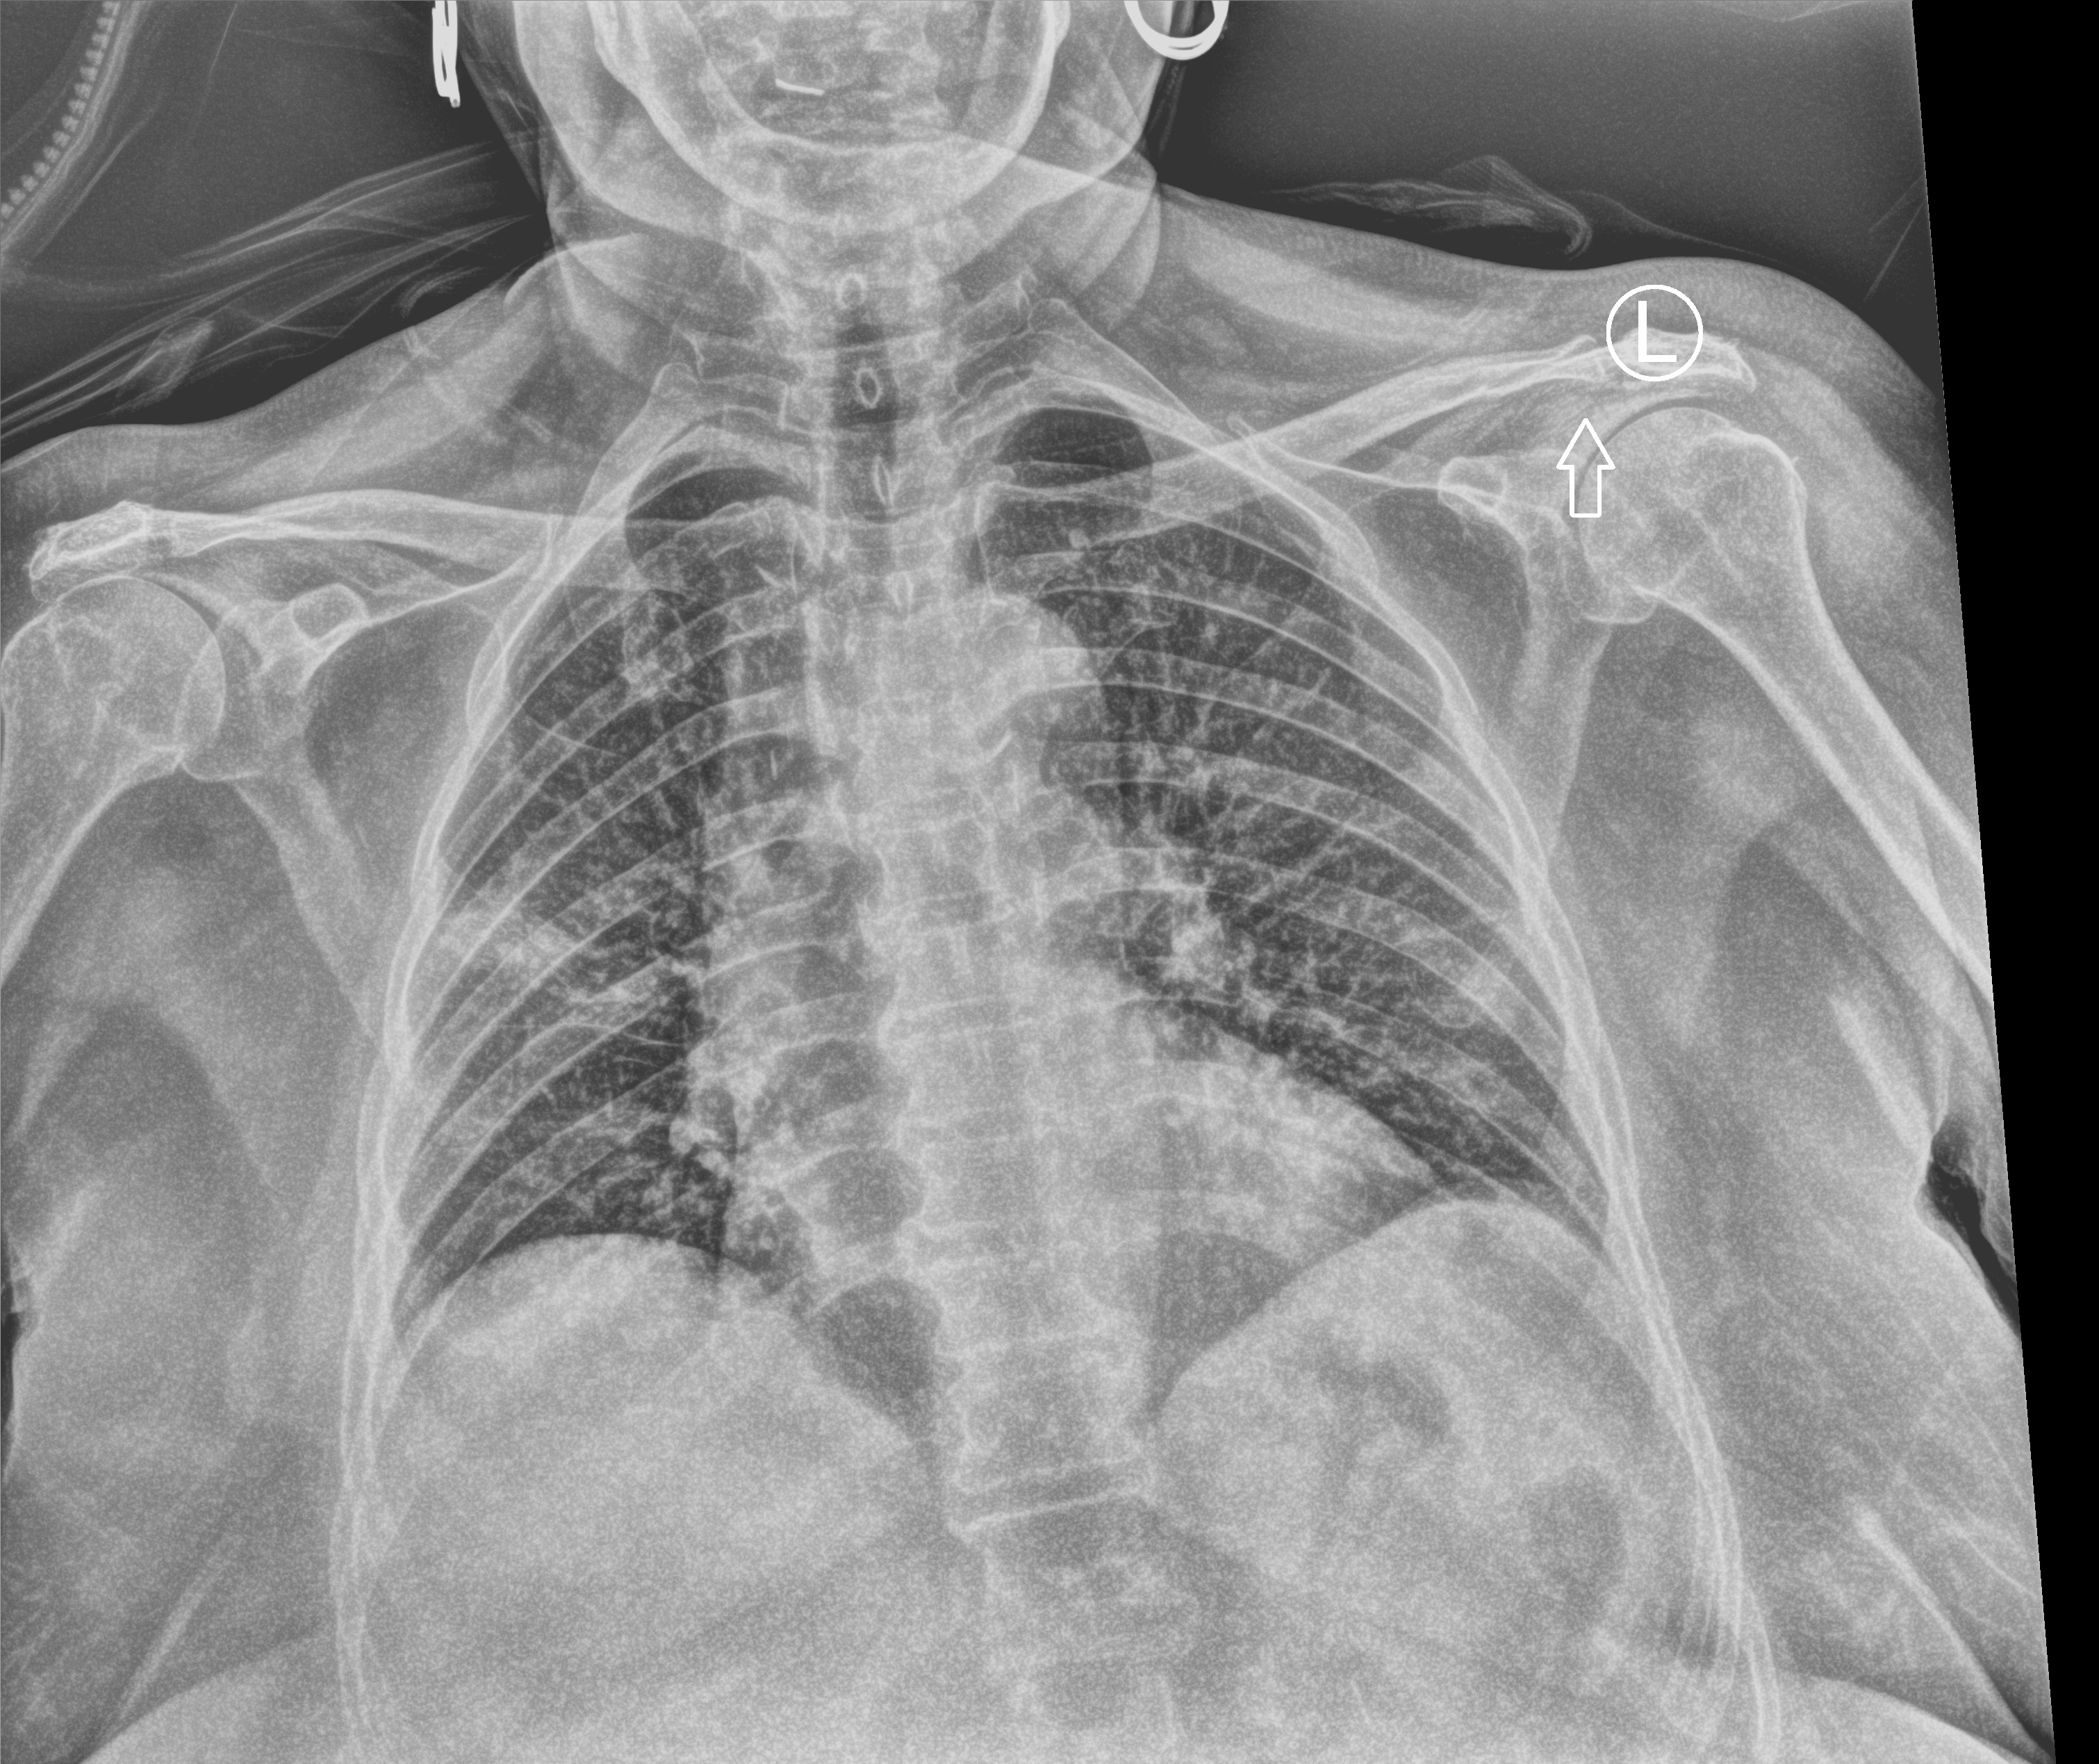
Bedside chest radiograph (computed radiography); anteroposterior (AP) projection. Patient hospitalised with COVID-19; female, aged 75–90 years.
From the hospital-stay record, not from the radiograph (when in the stay this image was taken is not recorded): COPD (admission record): no; mechanically ventilated during this hospital stay: no; admitted to intensive care during this hospital stay: no.